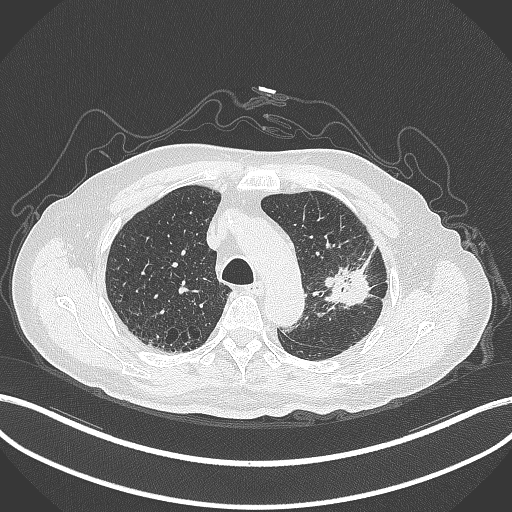
Chest CT, one axial slice. Position 220 of 331 along the scan axis. Reconstruction kernel B70f. Lung window (W 1500 / L -600 HU). 1 mm slice thickness. 512 × 512 image matrix, field of view 400 × 400 mm. Patient: male, 79 years. Case-level facts recorded for this patient, not image findings: clinical TNM (as recorded): T2a N1 M1; histopathological grade: G3.
Structures marked on this image (rectangle marked by the reading radiologist):
- lung tumour (recorded histology: adenocarcinoma): bounding box <325,244,381,311> (left, top, right, bottom; pixels)